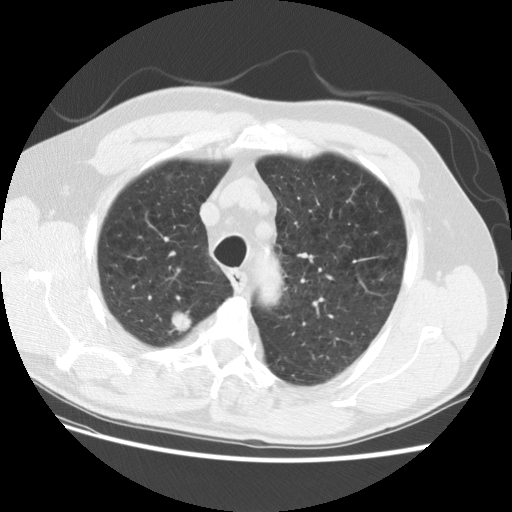
Chest CT (low-dose screening protocol), one axial image, baseline annual screen, lung window (W 1500 / L -600 HU), 2.5 mm slice thickness, standard (soft-tissue) reconstruction kernel (STANDARD), 140 kVp, slice 26 of 124 in the series, 512 × 512 image matrix. Male participant, aged 69 years at enrolment.
Expert reader's lesion annotation, box from (x=157, y=305) to (x=201, y=343) px. Screening reader's record for this exam (one nodule recorded; not confirmed to be the boxed lesion): non-calcified nodule or mass ≥4 mm, right upper lobe, 15 × 15 mm, spiculated (stellate) margins, soft tissue attenuation. Later outcome: lung cancer diagnosed 22 days after this screen — large cell neuroendocrine carcinoma, right upper lobe, poorly differentiated (G3), stage IA (AJCC 6th edition), 23 mm at pathology.